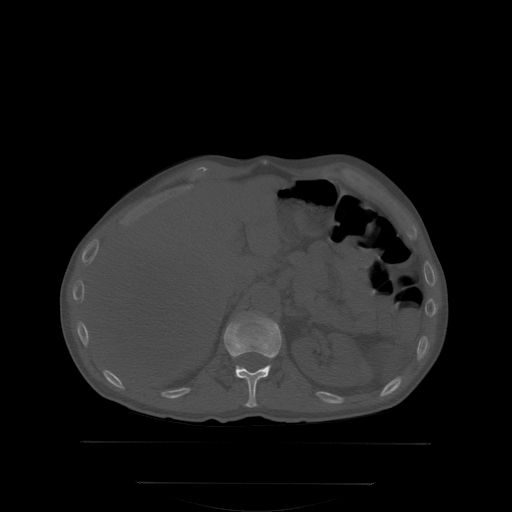
CT including the spine, one axial slice. Slice 165 of 350 in the series (ordered by position). Bone window (W 1800 / L 400 HU). 2.5 mm slice thickness. 512 × 512 image matrix. Male patient, age 58 years. From the clinical record (not read from this slice): primary cancer: prostate; vertebrae with lytic lesions (as recorded): L1.
Outlined on this slice (semi-automatic segmentation, software-assisted and operator-edited):
- T12 vertebra: bounding box <225,315,281,407> (left, top, right, bottom; pixels)